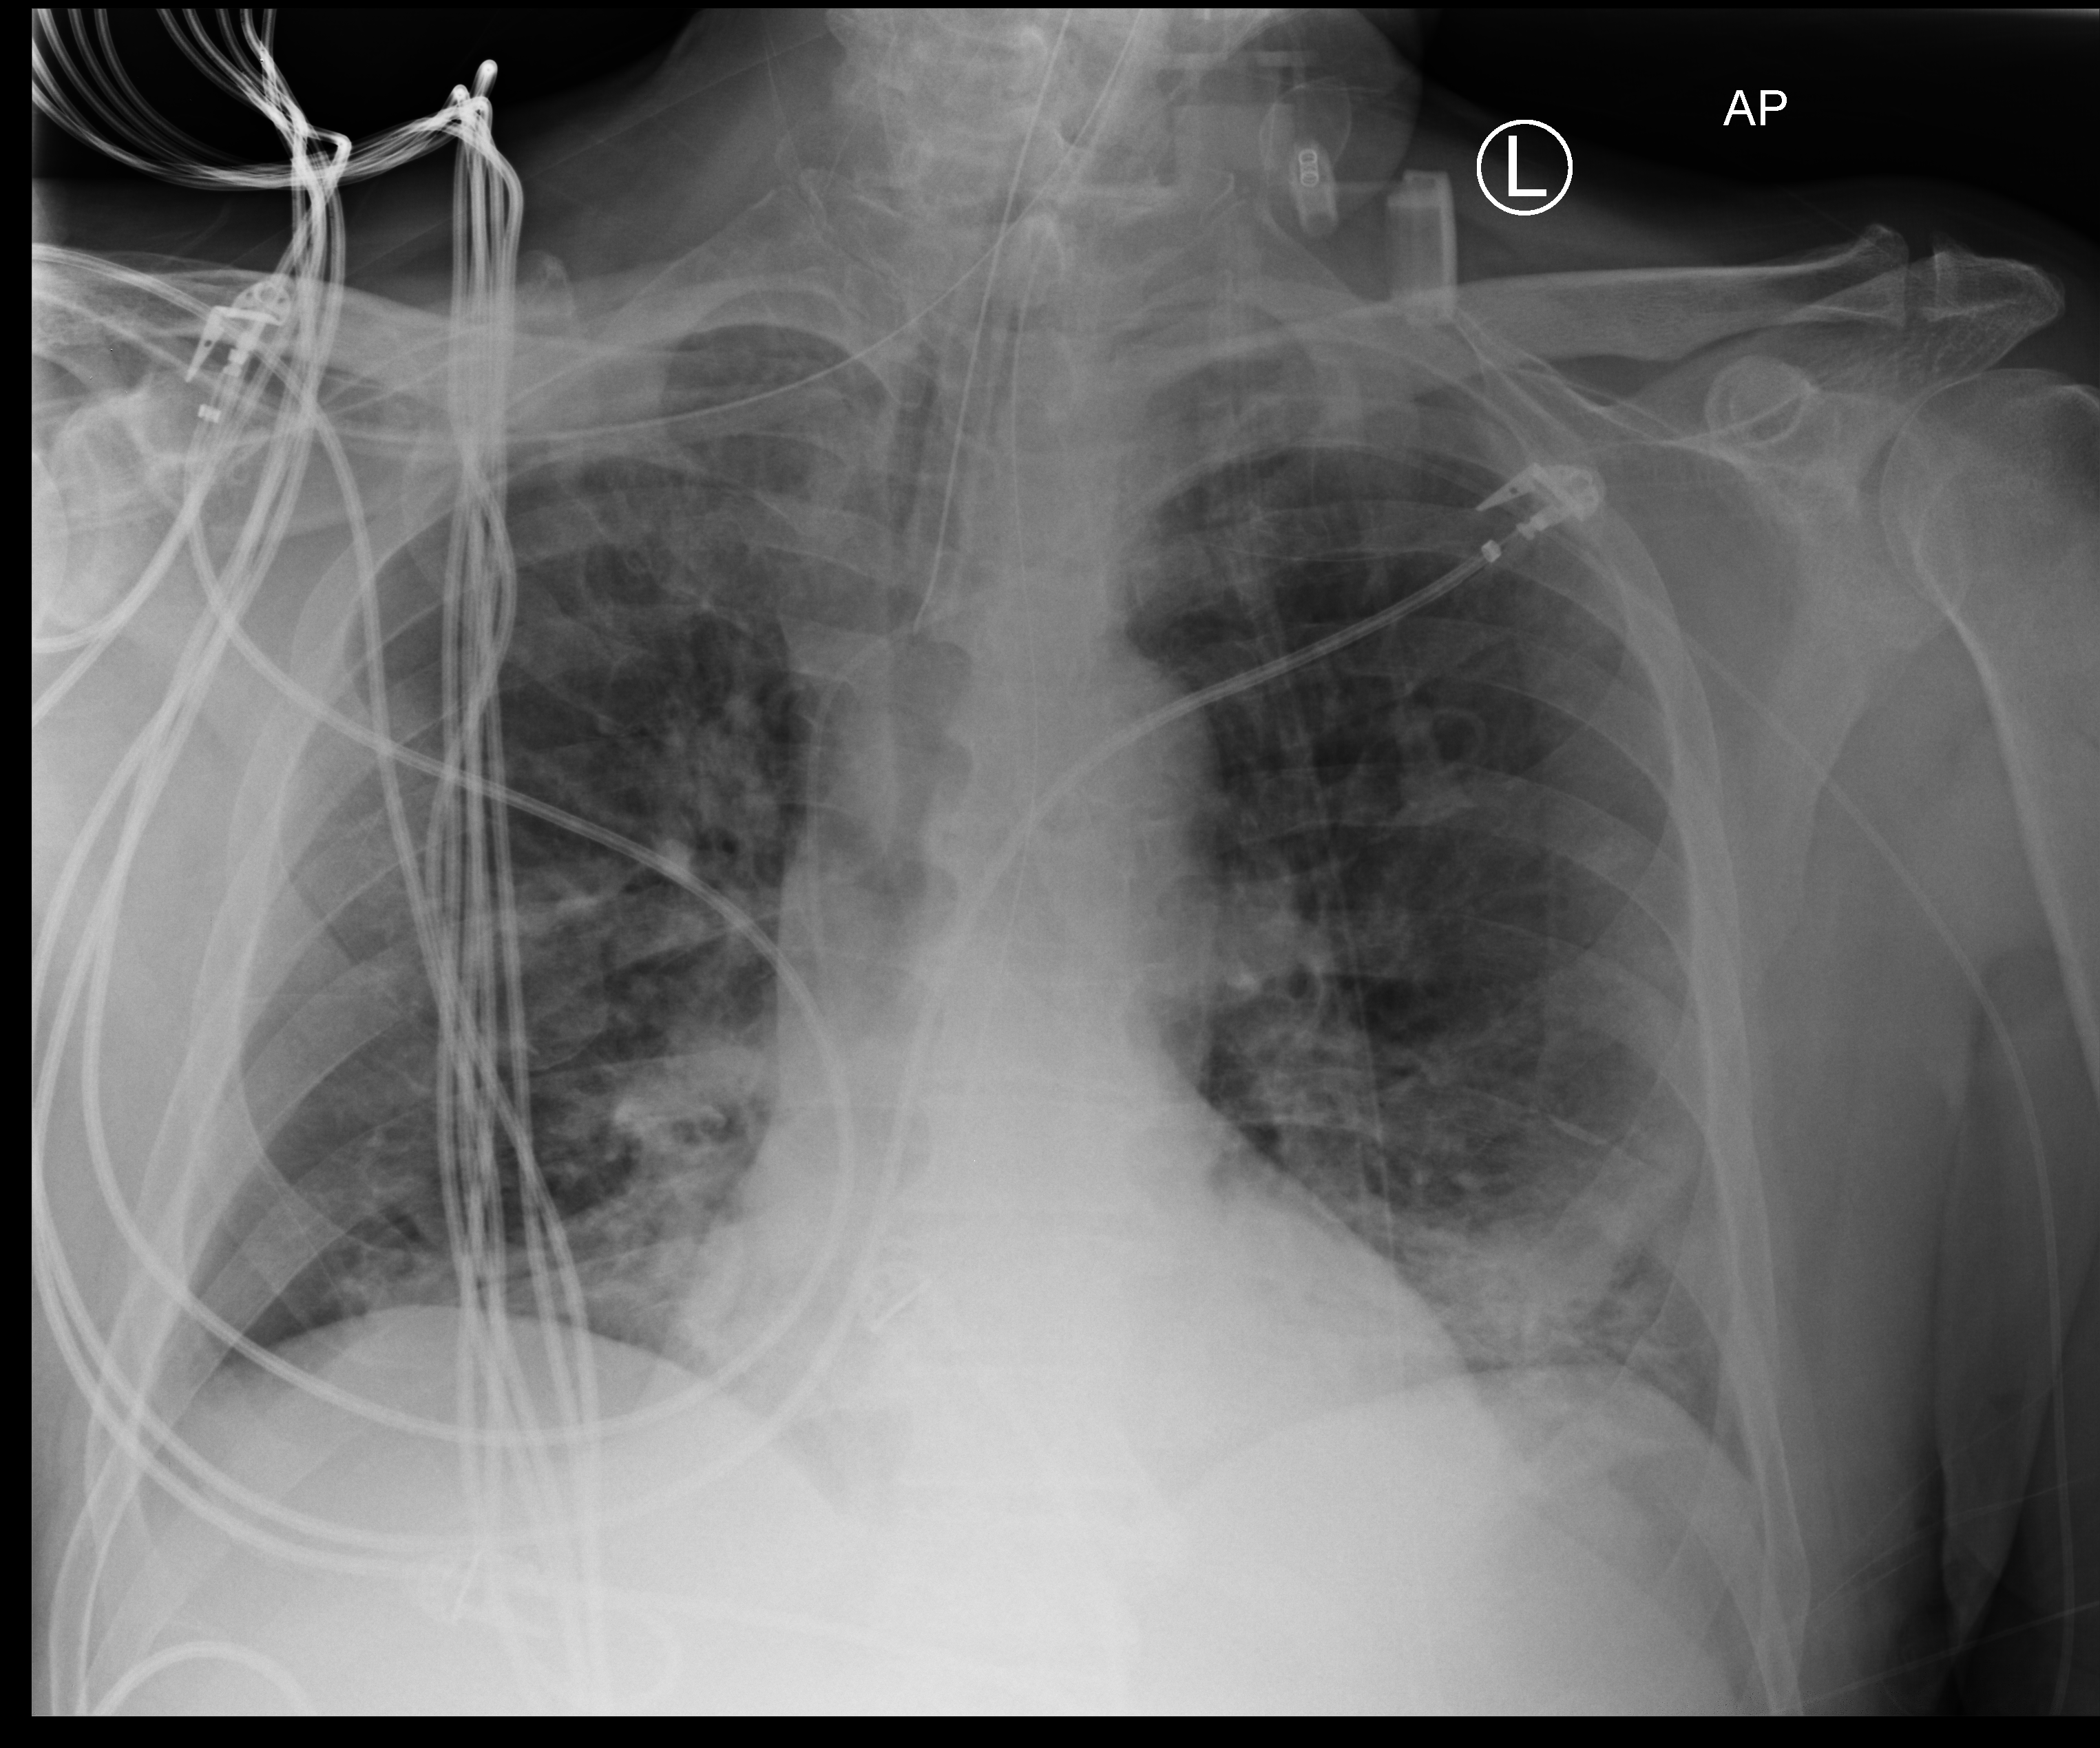
Portable chest radiograph, anteroposterior (AP) projection. Male patient hospitalised with COVID-19, age 60–74 years.
Admission-level facts for this patient (not findings on this image; timing relative to this image not recorded):
- mechanically ventilated during this hospital stay: yes
- admitted to intensive care during this hospital stay: yes
- other chronic lung disease (admission record): no